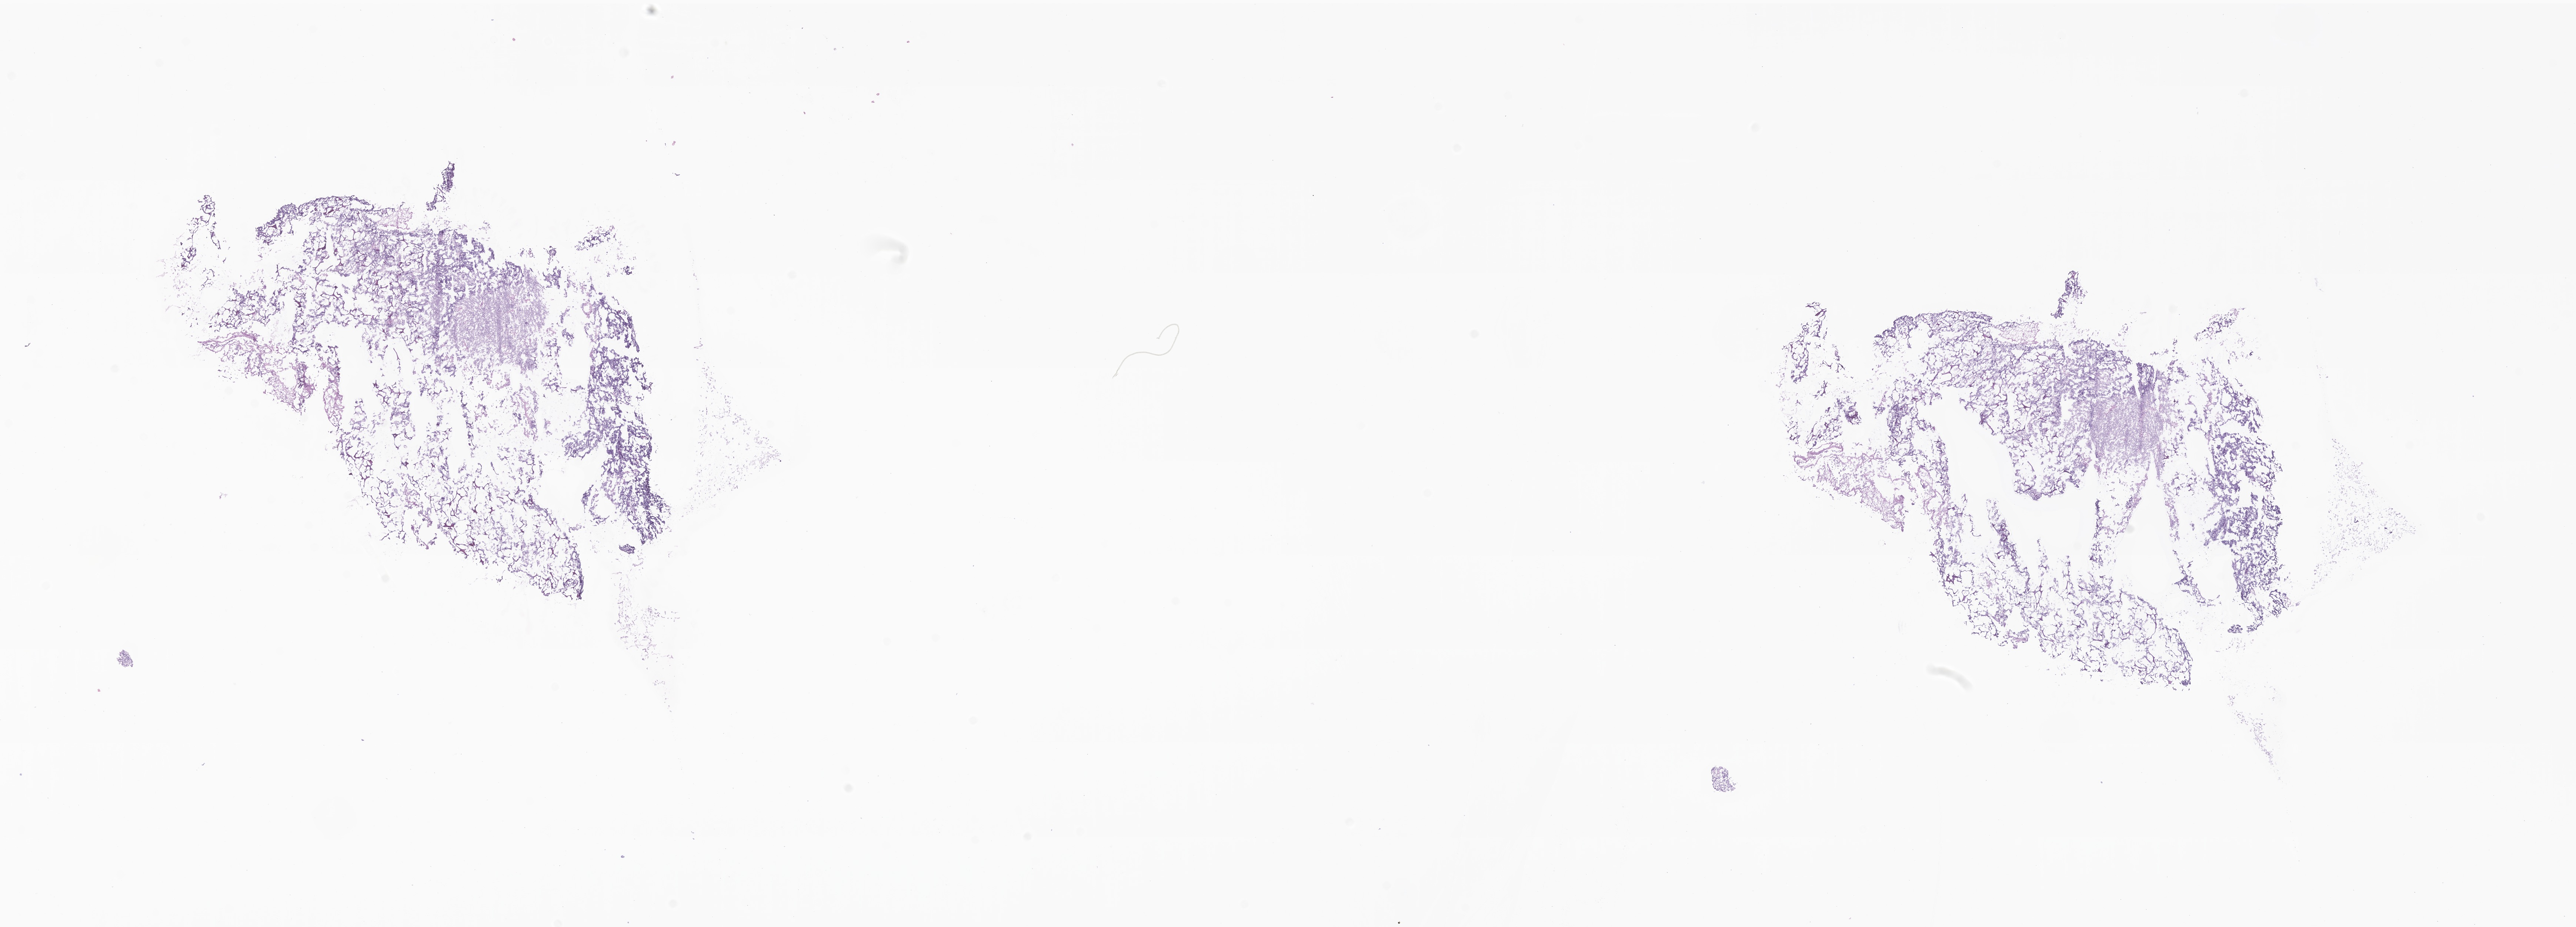
Whole-slide image, H&E stain of tumor tissue from the cerebellum, whole scanned area (about 29.3 x 10.5 mm) shown as a low-resolution overview. Cryosection (OCT / tissue freezing medium). Male patient, age 146 months.
• diagnosis: Neoplasm, uncertain whether benign or malignant